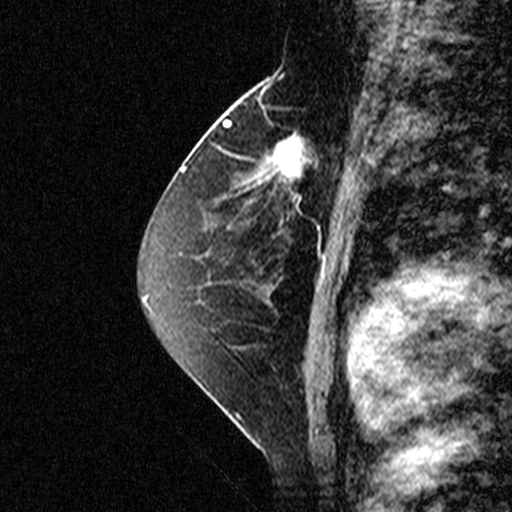
Breast MRI (dynamic contrast-enhanced), one sagittal slice. Slice 23 of 44 in the series (ordered by position). Dynamic contrast-enhanced study with each time point stored as its own series, time point 2 of 3 at this slice position (early post-contrast, ordered by acquisition time). 1.5 T. TE 4.5 ms, TR 11 ms. 3 mm slice thickness. 512 × 512 image matrix, field of view 200 × 200 mm. Female patient, age 49 years. Case-level facts recorded for this patient, not image findings: setting: breast cancer imaged before/during neoadjuvant chemotherapy; receptor status: triple-negative.
Outlined on this slice (semi-automatic segmentation, software-assisted and operator-edited):
- analysis volume of interest (the breast-tissue region the enhancement analysis was run in; not a lesion): bounding box (x1, y1, x2, y2) in pixels: (254, 112, 347, 207)
- tumour enhancement mask (voxels above the 90 % enhancement threshold inside the analysis volume of interest): (254, 112, 347, 207)